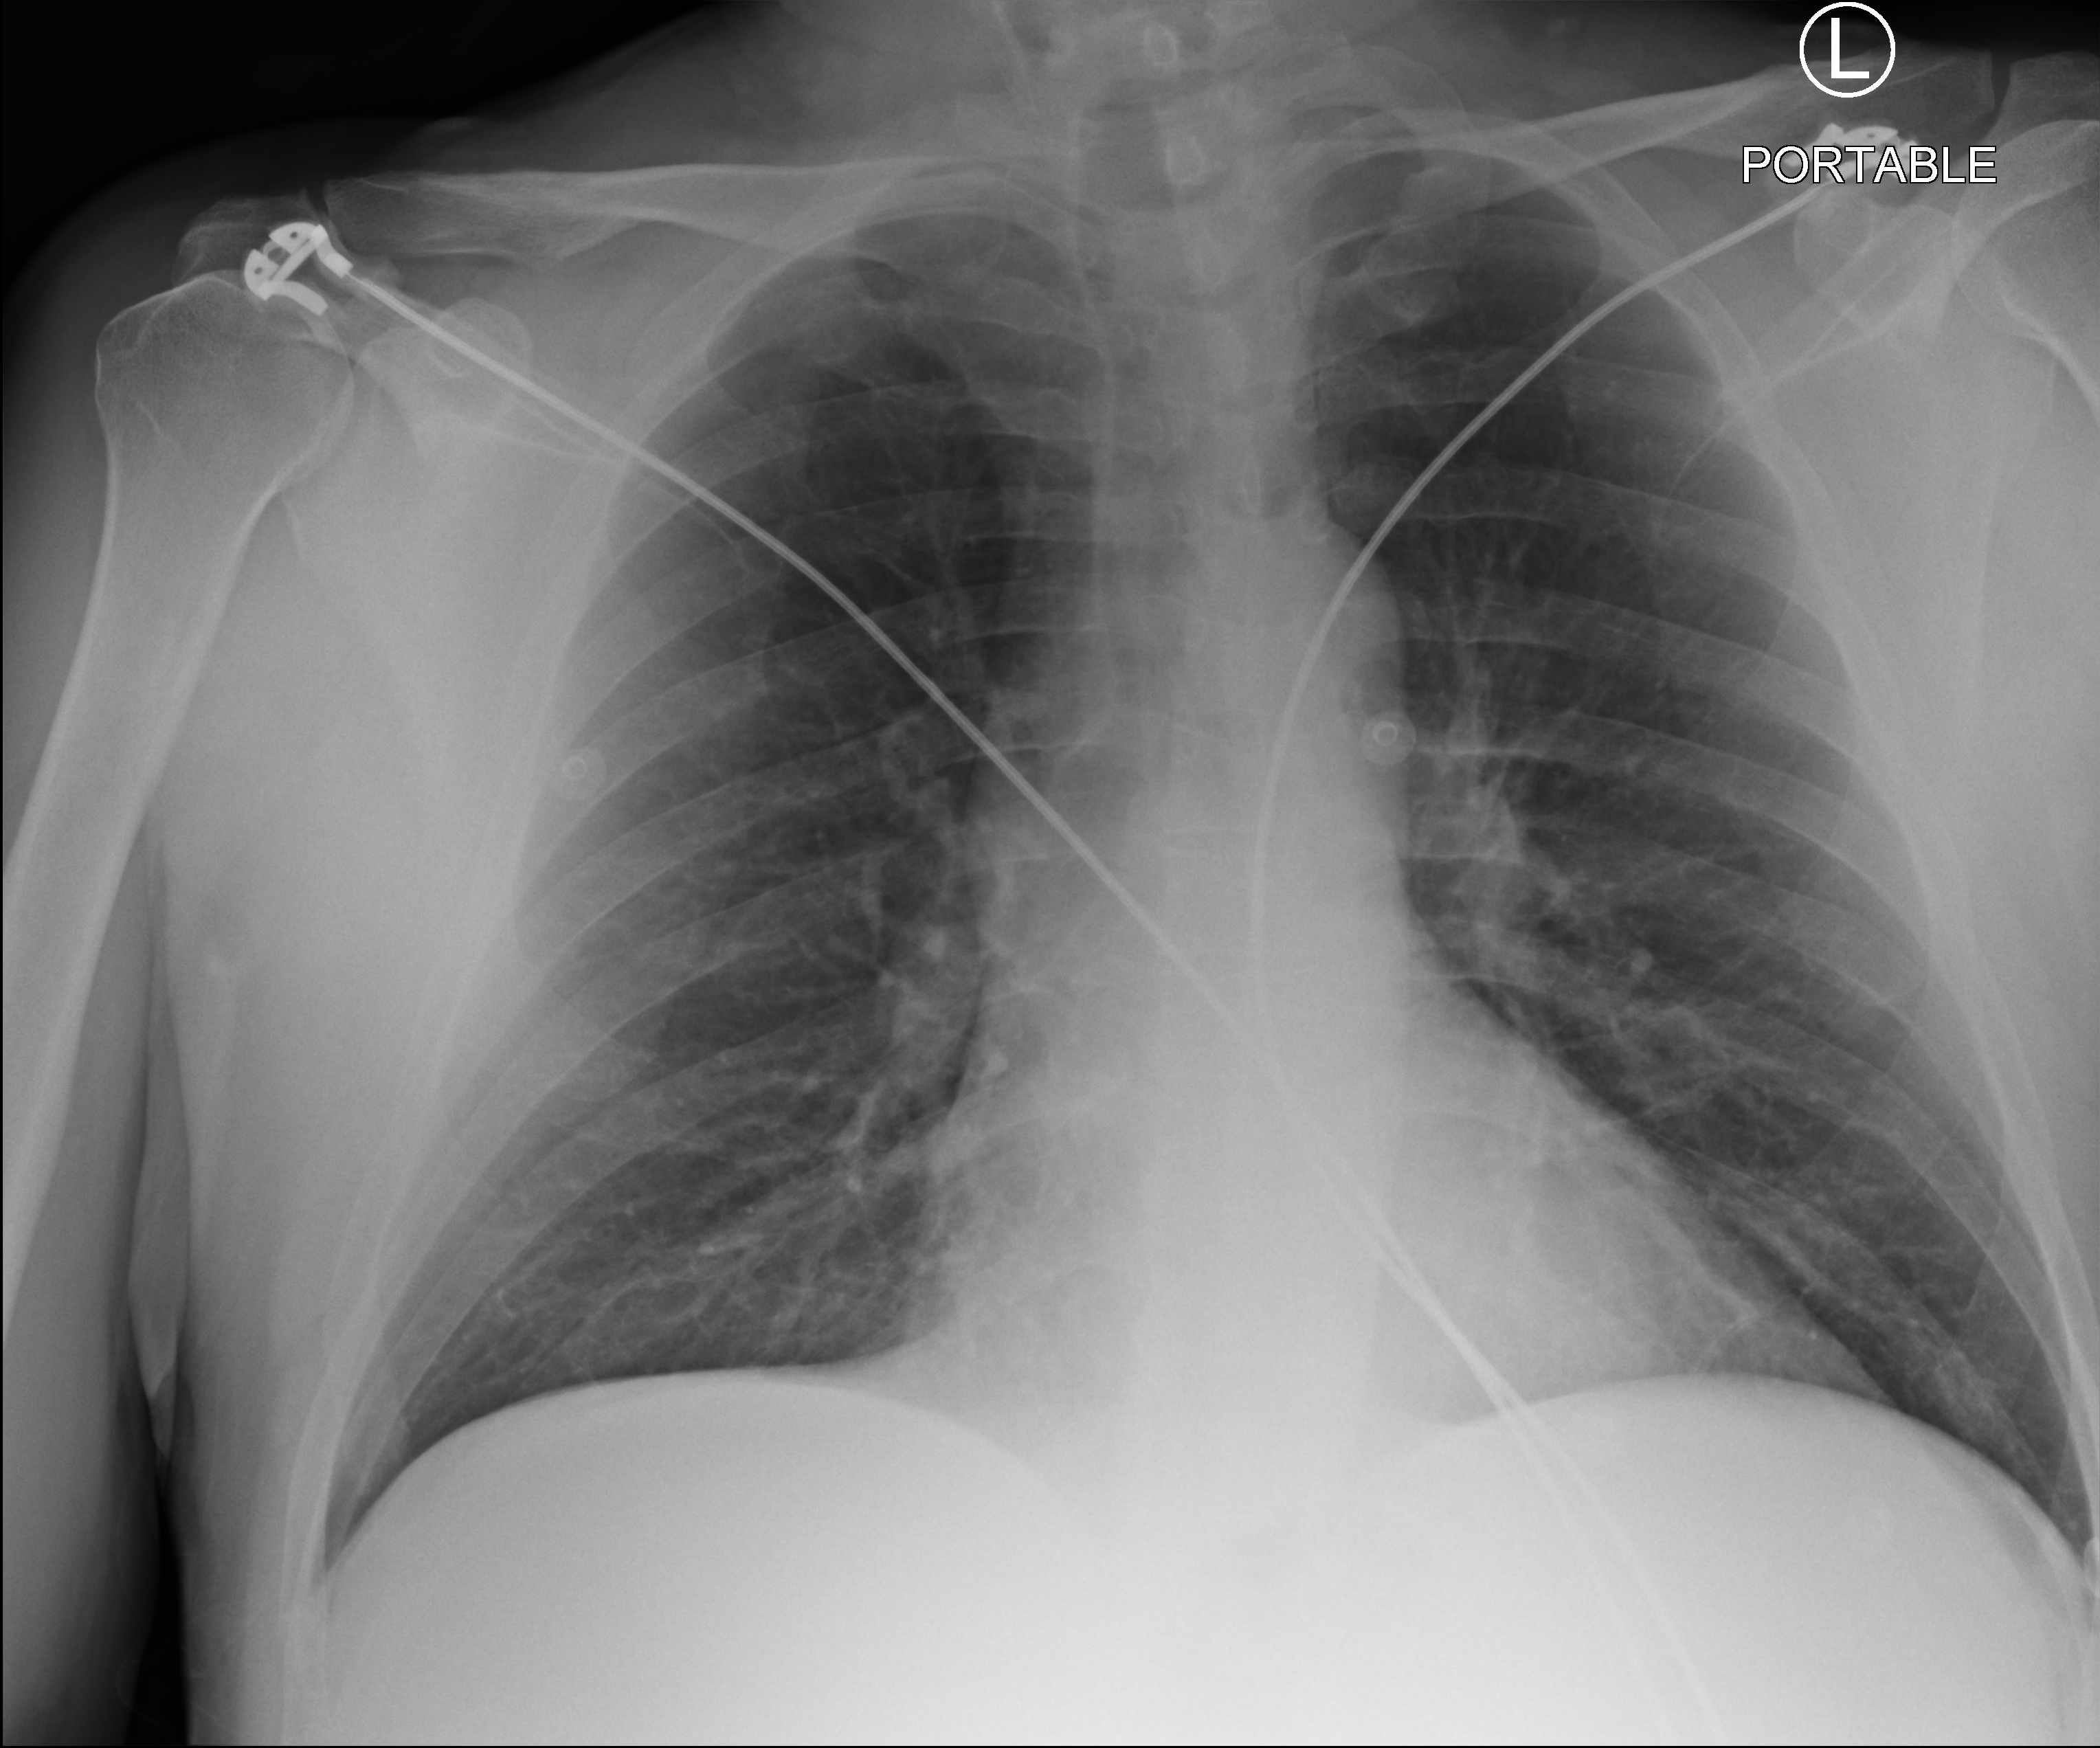
Portable chest radiograph; anteroposterior (AP) projection. Male patient hospitalised with COVID-19, age 18–59 years.
Admission-level facts for this patient (not findings on this image; timing relative to this image not recorded): admitted to intensive care during this hospital stay: no; diabetes (admission record): no; mechanically ventilated during this hospital stay: no.